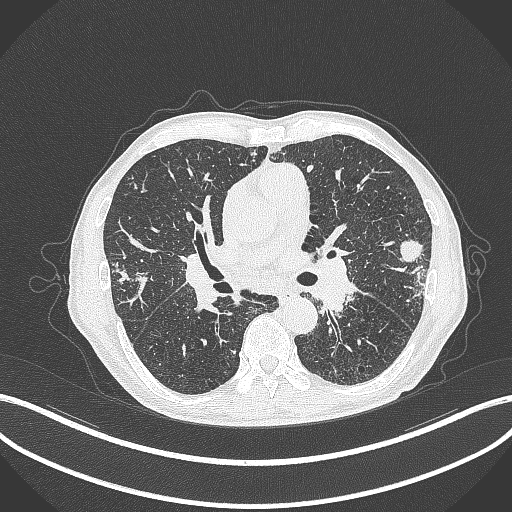
Chest CT, one axial slice; slice 221 of 463 in the series (ordered by position); 120 kVp; lung window (W 1500 / L -600 HU); 512 × 512 image matrix, field of view 400 × 400 mm. Male patient, age 74 years. From the clinical record (not read from this slice): clinical TNM (as recorded): T2a N1 M0.
Outlined on this slice (rectangle marked by the reading radiologist):
- lung tumour (recorded histology: adenocarcinoma): bounding box (x1, y1, x2, y2) in pixels: (395, 236, 435, 268)